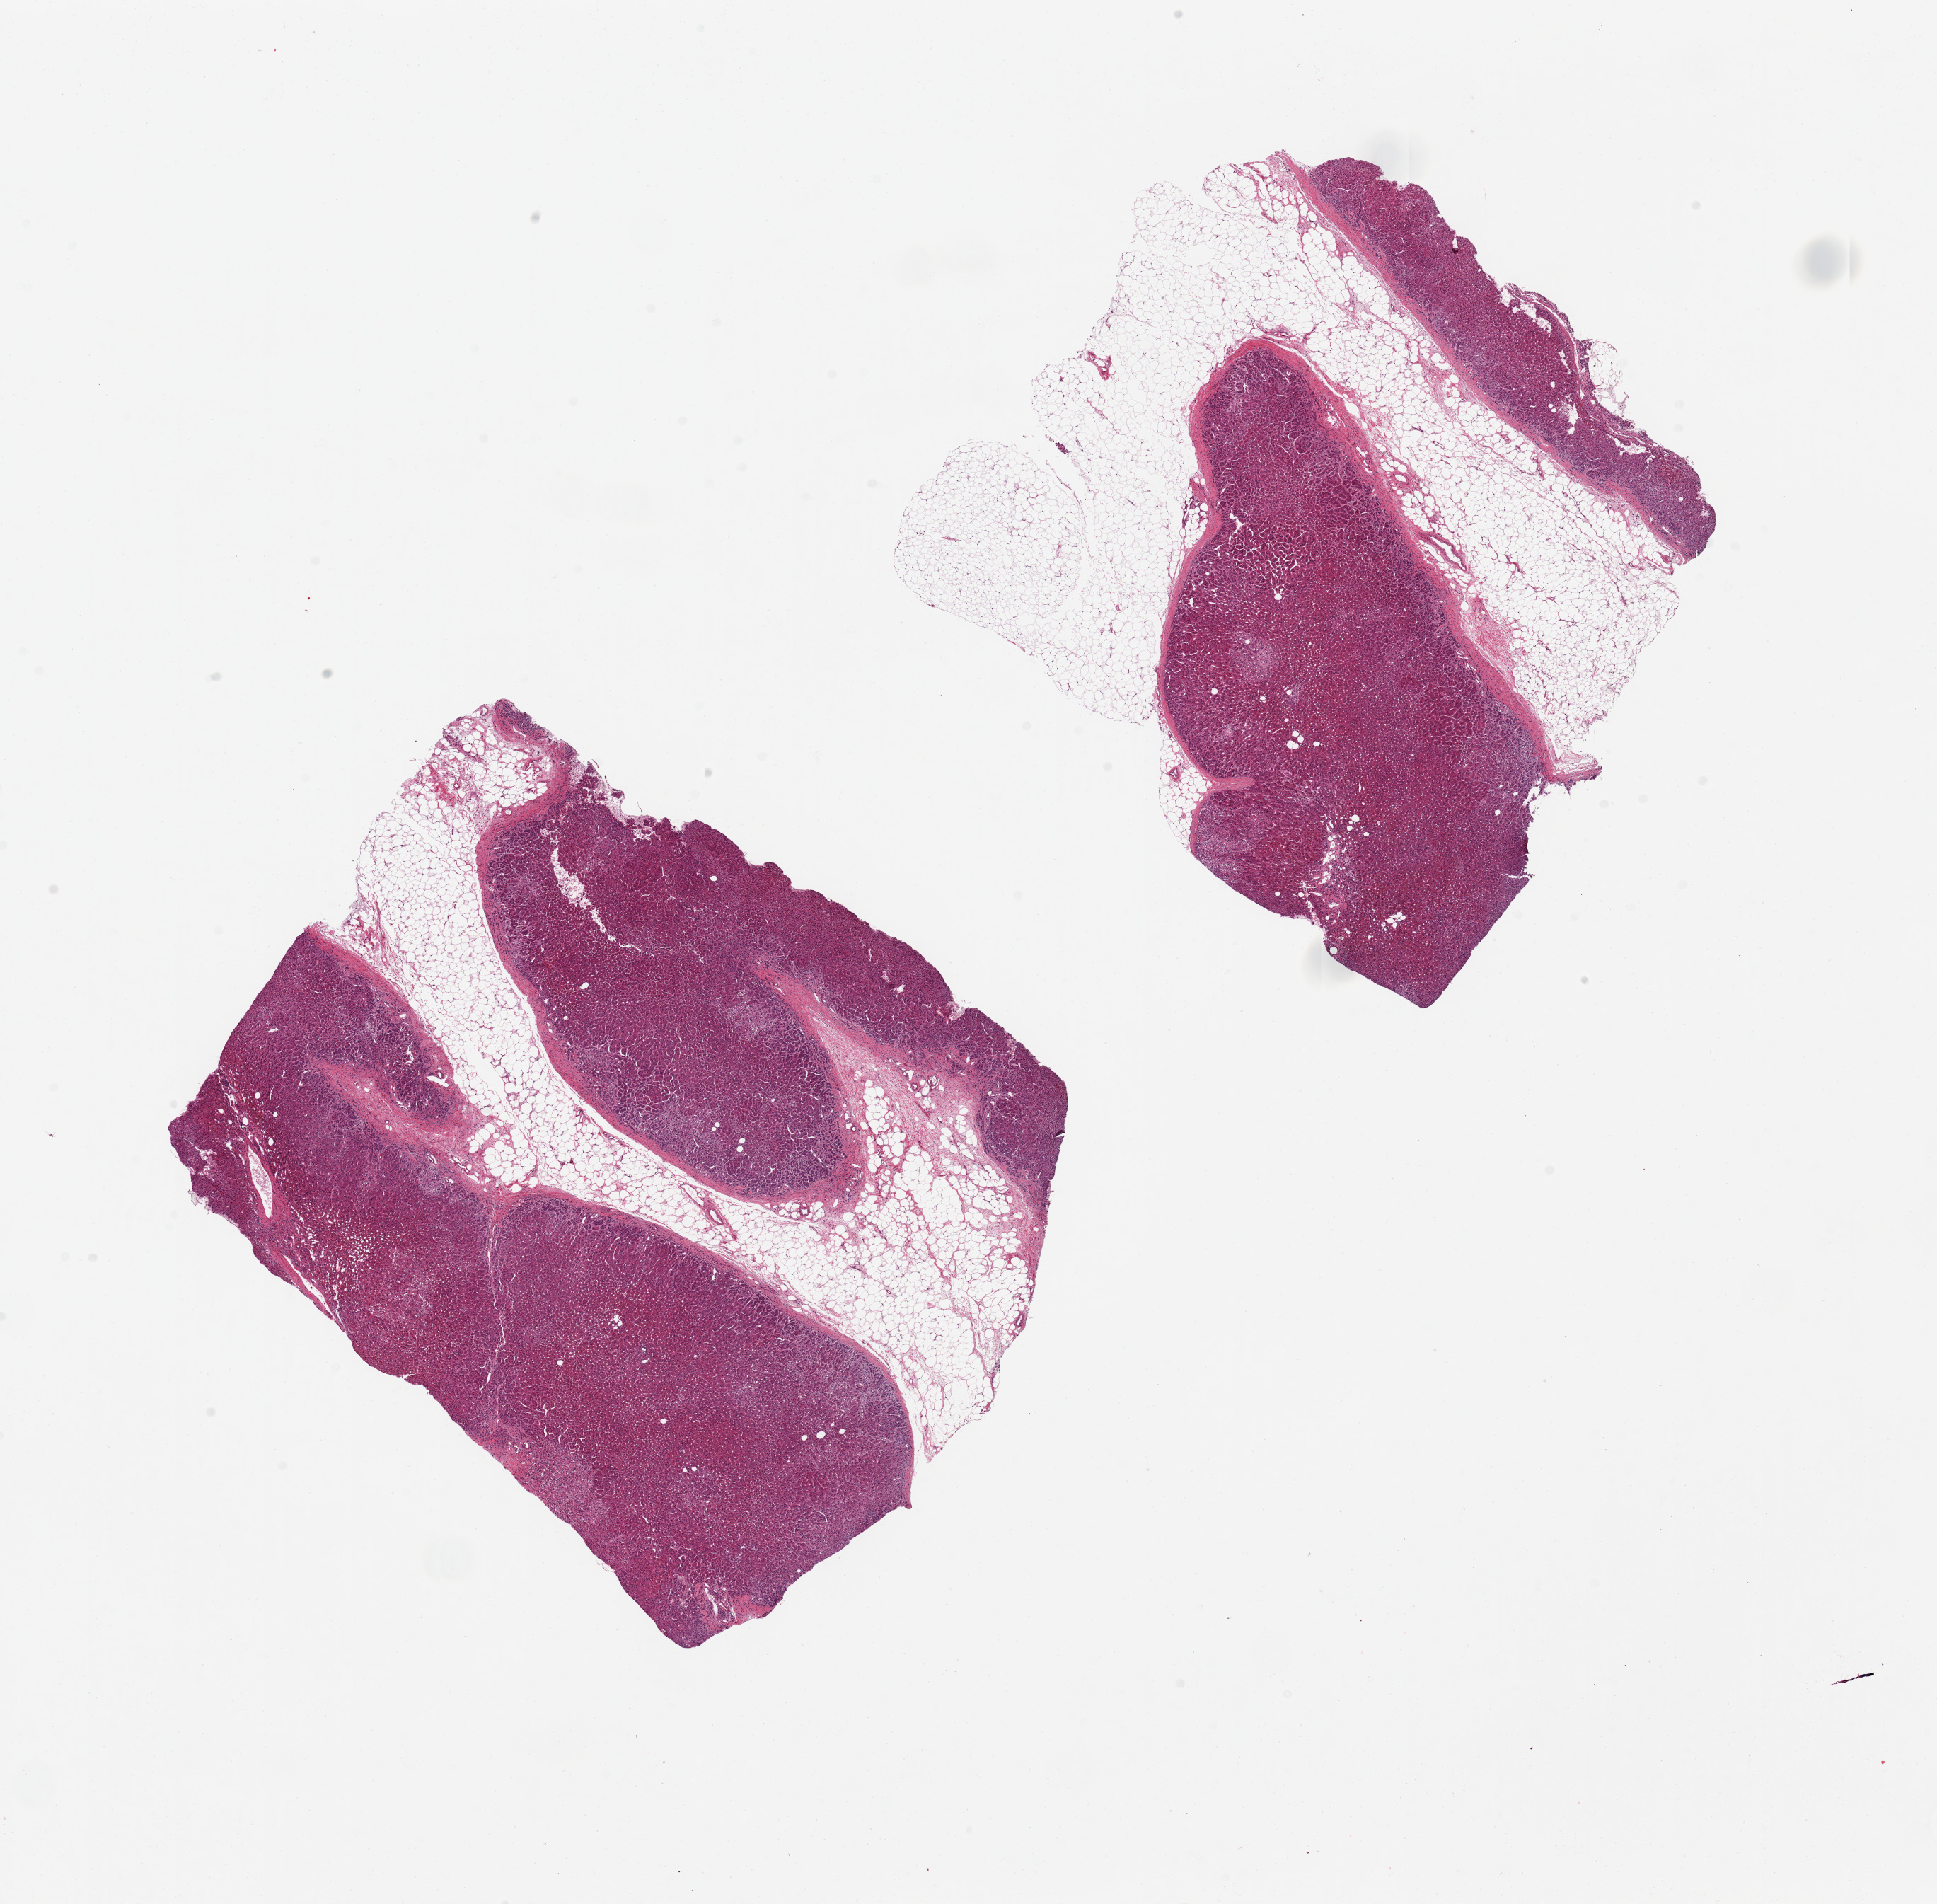
H&E whole-slide image, brightfield — shown as a low-resolution overview of the whole scanned area (about 21.7 x 21.3 mm). PAXgene-fixed paraffin-embedded (PFPE) section. Target tissue: adrenal gland. Tissue donor sample. Male donor.
Pathologist's review note for this sample: 2 pieces, 9x8 & 8x8mm; each has 30-40% adipose.